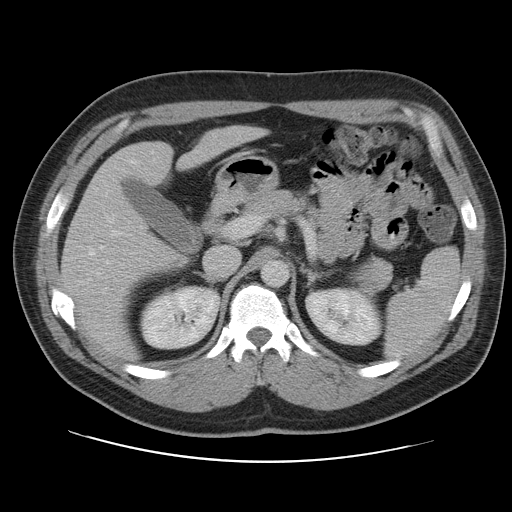
Contrast-enhanced abdominal CT, one axial slice; position 65 of 109 along the scan axis; 120 kVp; intravenous contrast given; soft-tissue window (W 400 / L 40 HU); 5 mm slice thickness; 512 × 512 image matrix. Male patient, age 35 years. From the clinical record (not read from this slice): diagnosis: colorectal cancer liver metastases, imaged before liver resection; multiple liver metastases: yes.
Structures marked on this image (expert manual segmentation):
- hepatic veins: bounding box (x1, y1, x2, y2) in pixels: (89, 252, 94, 255)
- liver: (62, 126, 260, 357)
- planned liver remnant (the part of the liver to remain after resection): (62, 126, 259, 358)
- portal vein (with intrahepatic branches): (81, 213, 140, 285)